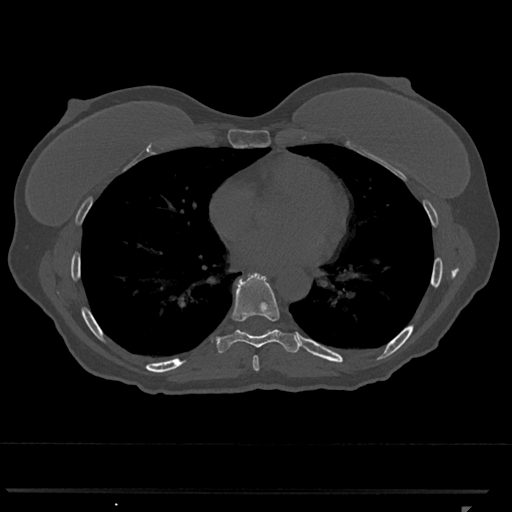
CT including the spine, one axial slice; position 665 of 793 along the scan axis; 120 kVp; bone window (W 1800 / L 400 HU); 0.5 mm slice thickness; 512 × 512 image matrix, field of view 380 × 380 mm. Patient: female, 62 years. From the clinical record (not read from this slice): primary cancer: renal.
Outlined on this slice (semi-automatic segmentation, software-assisted and operator-edited):
- T7 vertebra: bounding box [x1, y1, x2, y2] px = [252, 356, 260, 371]
- T8 vertebra: [216, 272, 301, 353]